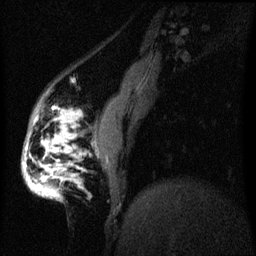
Breast MRI (dynamic contrast-enhanced), one sagittal slice. Slice 12 of 60 in the series (ordered by position). Dynamic contrast-enhanced series, image 2 of 3 at this slice position (ordered by acquisition). 1.5 T. TE 4.2 ms, TR 8 ms. 2.2 mm slice thickness. 256 × 256 image matrix, field of view 200 × 200 mm. Female patient, age 50 years.
Annotated regions visible in this slice (semi-automatic segmentation, software-assisted and operator-edited):
- analysis volume of interest (the breast-tissue region the enhancement analysis was run in; not a lesion): bounding box (x1, y1, x2, y2) in pixels: (21, 112, 70, 201)
- tumour enhancement mask (voxels above the 70 % enhancement threshold inside the analysis volume of interest): (25, 120, 67, 191)